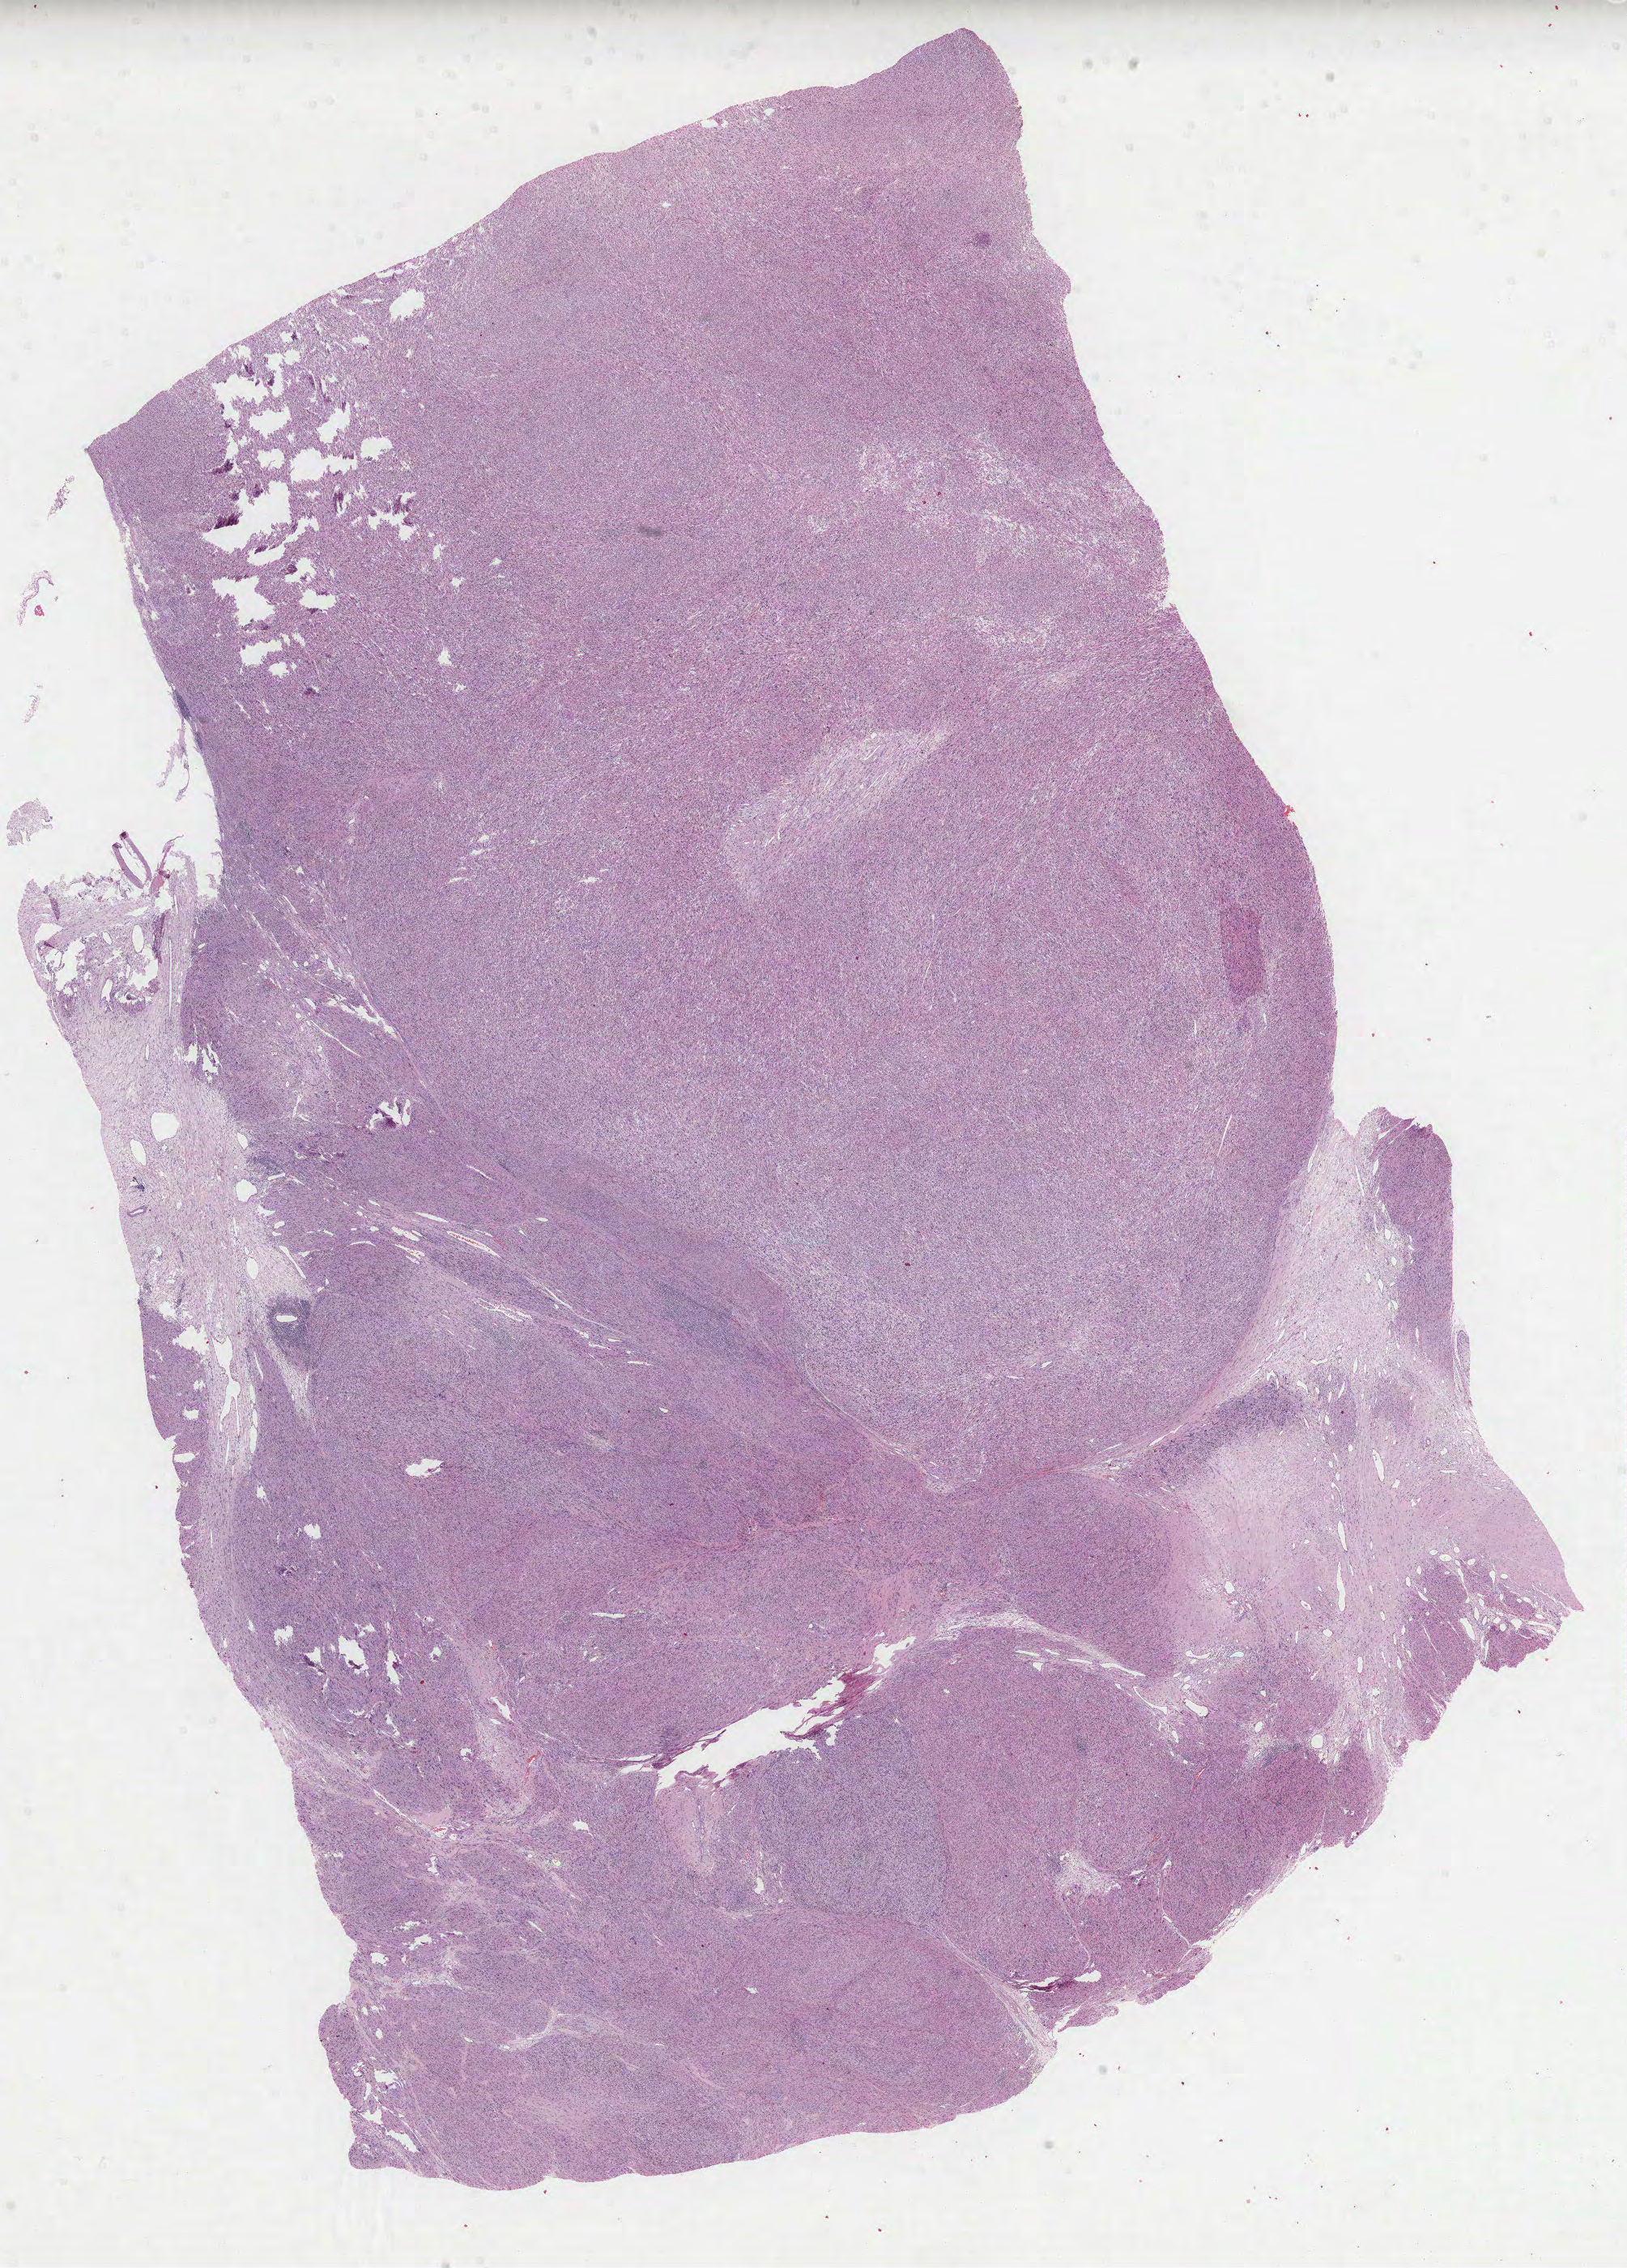
H&E whole-slide image, whole scanned area (about 16.2 x 22.6 mm, slide scanned at 40x) shown as a low-resolution overview, formalin-fixed paraffin-embedded (FFPE) diagnostic section, sample: primary tumour, retroperitoneum and peritoneum. Female patient; age at initial diagnosis 66 years.
Diagnosis: Leiomyosarcoma, NOS (retroperitoneum).